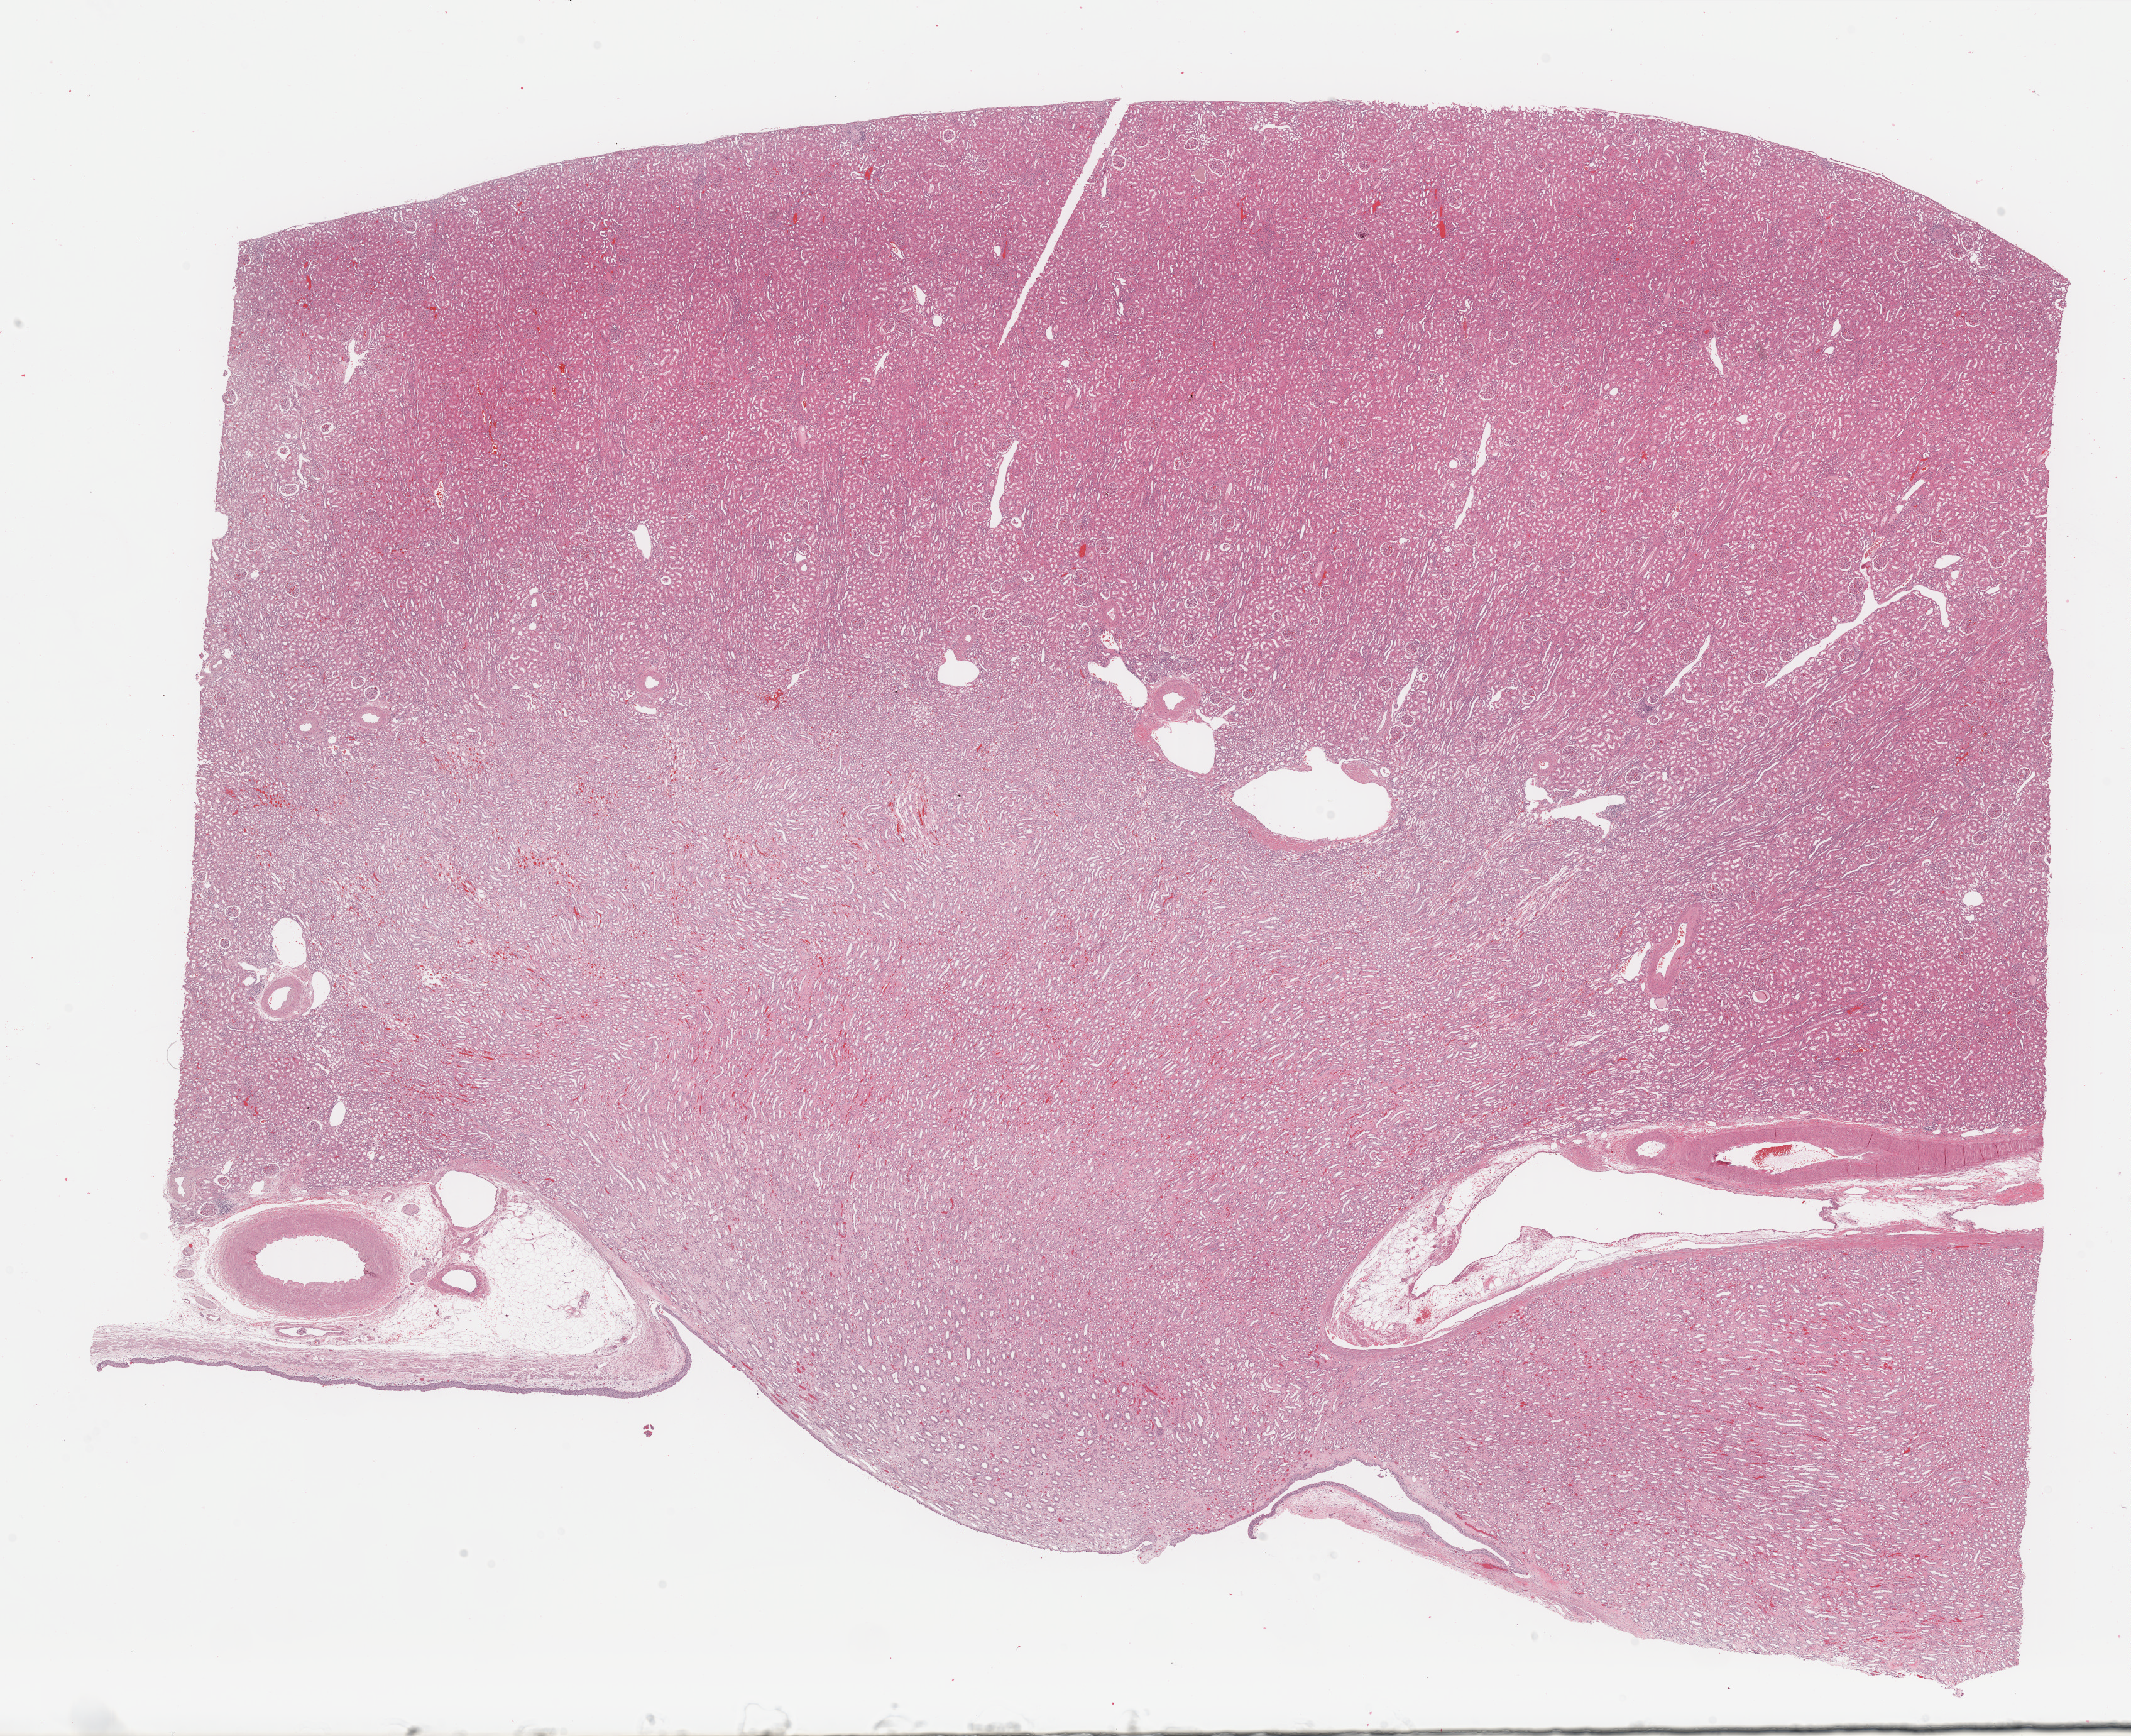
Digitized H&E tissue section (whole slide), shown as a low-resolution overview of the whole scanned area (about 26.8 x 21.9 mm). FFPE section. Kidney, solid tissue normal (non-tumour tissue) sample. Female patient; age at initial diagnosis 44 years. Pathologist review of this section (percent, as recorded): tumour cells 0%, tumour nuclei 0%, normal cells 60%, stromal cells 40%, necrosis 0%. Infiltration values recorded for this section: lymphocyte infiltration 0%, monocyte infiltration 0%, neutrophil infiltration 0%.
This section: solid tissue normal sample (biorepository sample class). Patient diagnosis: Renal cell carcinoma, chromophobe type.